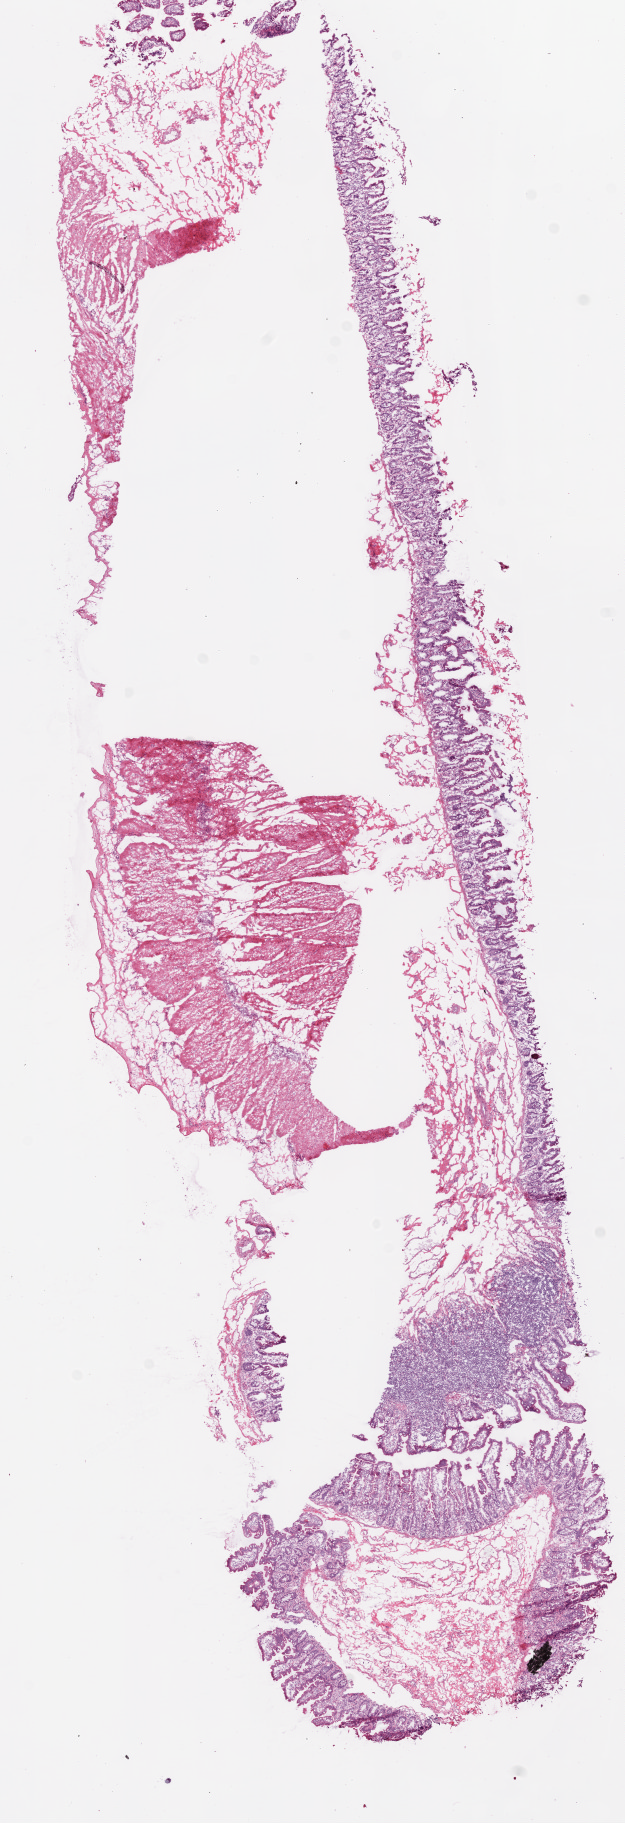
Digitized Hematoxylin and eosin (H&E) stained tissue section (whole slide), shown as a low-resolution overview of the whole scanned area (about 5.0 x 14.6 mm, slide scanned at 20x); frozen section from the bottom of the tissue portion; solid tissue normal (non-tumour tissue) sample from the ovary. Female patient; age at initial diagnosis 61 years.
This section: solid tissue normal sample (biorepository sample class). Patient diagnosis: Serous cystadenocarcinoma, NOS.